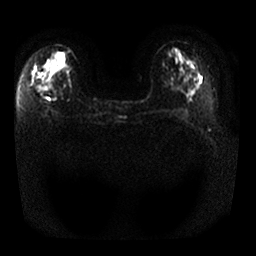
Breast MRI, one axial slice. Position 10 of 25 along the scan axis. Diffusion-weighted series; image 2 of 4 stored at this slice position (different b-values; order by instance number). 1.5 T. 4 mm slice thickness. 256 × 256 image matrix, field of view 340 × 340 mm. Female patient.
Structures marked on this image (outlined manually by an expert reader):
- tumour on diffusion-weighted imaging: box from (x=34, y=77) to (x=41, y=84) px